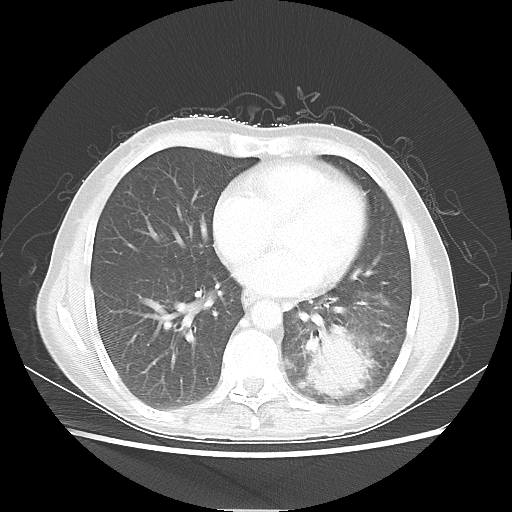
Chest CT, one axial slice; position 23 of 56 along the scan axis; reconstruction kernel LUNG; 80 kVp; lung window (W 1500 / L -600 HU); 512 × 512 image matrix, field of view 360 × 360 mm. Female patient, age 53 years. Case-level facts recorded for this patient, not image findings: clinical TNM (as recorded): T3 N0 M0.
Annotated regions visible in this slice (rectangle marked by the reading radiologist):
- lung tumour (recorded histology: adenocarcinoma): box from (x=304, y=325) to (x=379, y=399) px